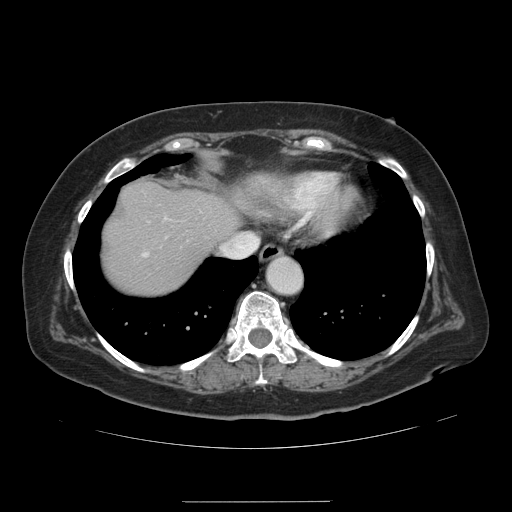
Contrast-enhanced abdominal CT, one axial slice. Position 120 of 141 along the scan axis. 120 kVp. Intravenous contrast given. Soft-tissue window (W 400 / L 40 HU). 2.5 mm slice thickness. 512 × 512 image matrix, field of view 393 × 393 mm. Female patient, age 74 years. From the clinical record (not read from this slice): diagnosis: colorectal cancer liver metastases, imaged before liver resection; multiple liver metastases: yes; largest metastasis: 7 cm; disease in both lobes: yes.
Annotated regions visible in this slice (manually delineated by an expert):
- hepatic veins: bounding box [x1, y1, x2, y2] px = [221, 233, 250, 250]
- liver: [105, 183, 239, 293]
- planned liver remnant (the part of the liver to remain after resection): [105, 183, 239, 293]